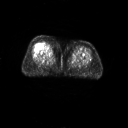
FDG PET of an extremity soft-tissue mass (from a PET/CT study), one axial slice; slice 22 of 267 in the series (ordered by position); 3.27 mm slice thickness; 128 × 128 image matrix, field of view 700 × 700 mm. Patient: female, 56 years. Case-level facts recorded for this patient, not image findings: histological type: malignant solitary fibrous tumor; grade: intermediate; site of the primary tumour: right thigh.
Outlined on this slice (expert contour drawn on MRI and transferred to this co-registered scan by the dataset authors):
- gross tumour volume including surrounding oedema: box from (x=39, y=41) to (x=54, y=53) px